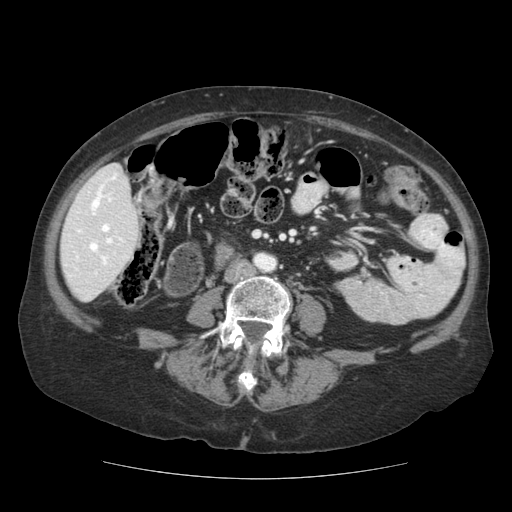
Contrast-enhanced abdominal CT (liver protocol), one axial slice. Position 35 of 111 along the scan axis. Reconstruction kernel STANDARD. 140 kVp. Soft-tissue window (W 400 / L 40 HU). 512 × 512 image matrix. Case-level facts recorded for this patient, not image findings: diagnosis: hepatocellular carcinoma (patient treated with transarterial chemoembolisation; whether this scan precedes or follows treatment is not stated here); TNM stage (as recorded): Stage-I; Child-Pugh class: A; tumour nodularity: uninodular; tumour size: 7.3 cm.
Annotated regions visible in this slice (semi-automatically segmented with operator editing):
- liver parenchyma outside the tumour (the mass and vessels are separate outlines, so this box may not span the whole liver): bounding box (x1, y1, x2, y2) in pixels: (60, 164, 140, 301)
- liver vessels: (75, 173, 127, 275)